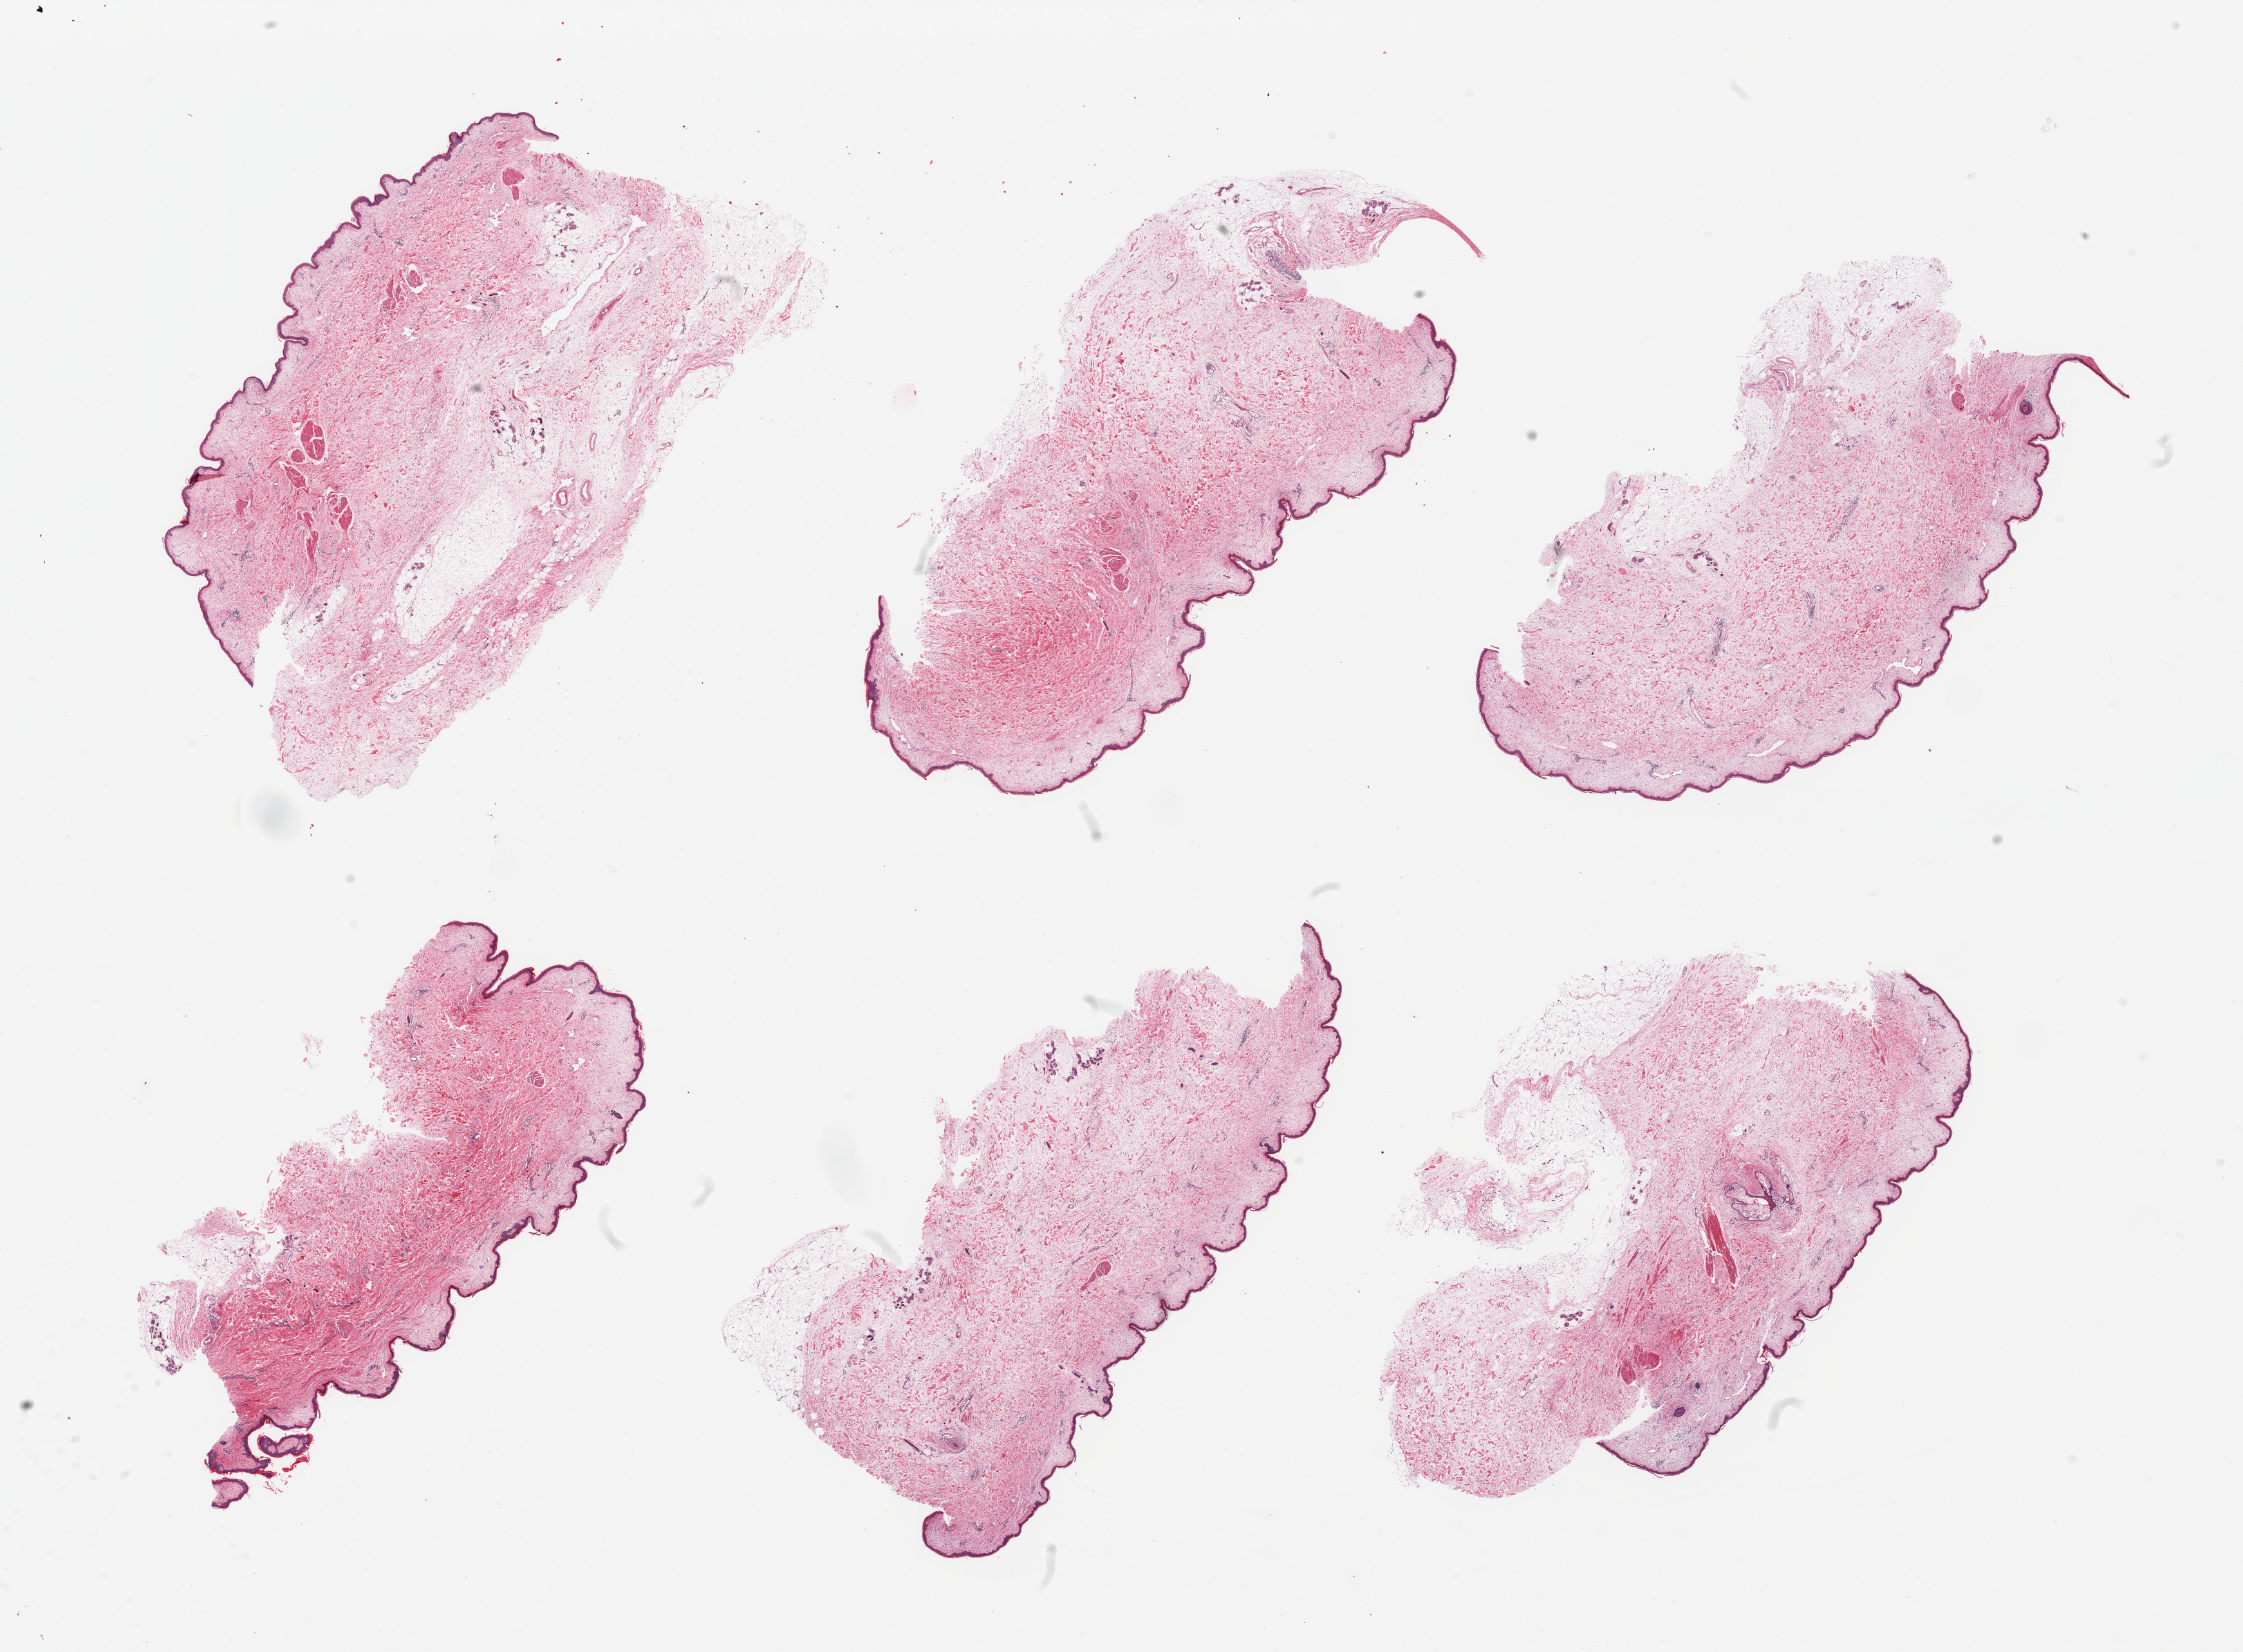
Hematoxylin and eosin (H&E) whole-slide image — a low-resolution overview of the entire scanned area, about 27.6 x 20.3 mm; PAXgene-fixed, paraffin-embedded tissue; target tissue: skin of suprapubic region; donor tissue sample.
Reviewer comment on this tissue sample: 6 pieces, squamous epithelium is ~30-35 microns; focal adherent dermal fat.